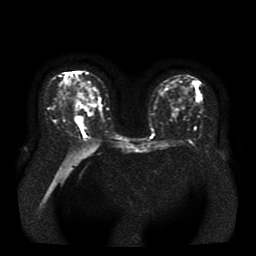
Breast MRI, one axial slice; slice 18 of 41 in the series (ordered by position); diffusion-weighted series; image 2 of 4 stored at this slice position (different b-values; order by instance number); 1.5 T; 5 mm slice thickness; 256 × 256 image matrix, field of view 330 × 330 mm. Female patient.
Outlined on this slice (manually delineated by an expert):
- tumour on diffusion-weighted imaging: bounding box <81,118,84,122> (left, top, right, bottom; pixels)